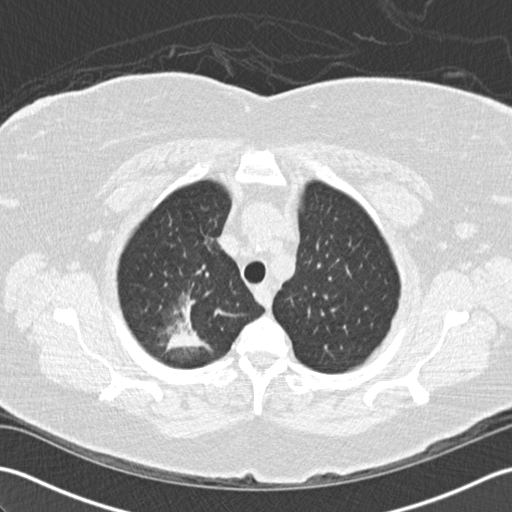
Chest CT (low-dose screening protocol), one axial image; first (baseline) screen; lung window (W 1500 / L -600 HU); 2 mm slice thickness; slice 25 of 156 in the series. Female participant, aged 72 years at enrolment.
Lesion marked by an expert reader, bounding box [x1, y1, x2, y2] px = [137, 276, 230, 368]. The screening reader recorded 2 non-calcified nodules or masses ≥4 mm on this exam; which of them this box marks is not recorded. Official screen result: positive, change unspecified: nodule(s) >= 4 mm or enlarging nodule(s), mass(es), or other non-specific abnormalities suspicious for lung cancer. Participant outcome: lung cancer diagnosed 494 days after this screen (after the second annual screen) — bronchiolo-alveolar adenocarcinoma, NOS, right upper lobe, stage IIIB (AJCC 6th edition), 45 mm at pathology.